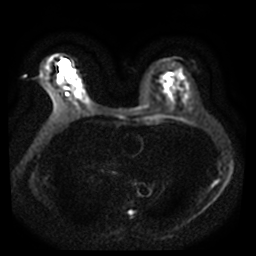
Breast MRI, one axial slice; position 20 of 42 along the scan axis; diffusion-weighted series; image 2 of 4 stored at this slice position (different b-values; order by instance number); 3 T; 5 mm slice thickness; 256 × 256 image matrix, field of view 340 × 340 mm. Female patient.
Structures marked on this image (outlined manually by an expert reader):
- tumour on diffusion-weighted imaging: bounding box <60,60,70,72> (left, top, right, bottom; pixels)